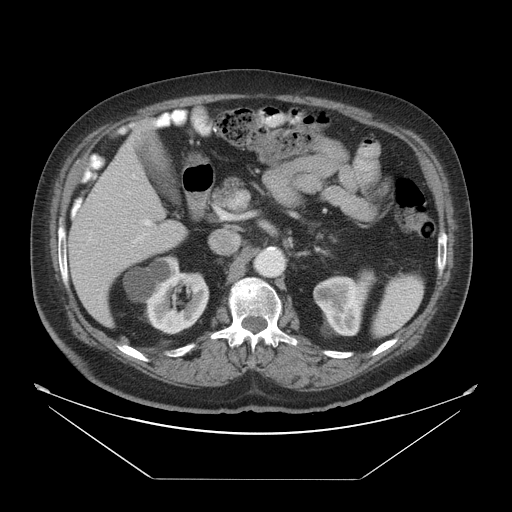
Contrast-enhanced abdominal CT, one axial slice. Position 25 of 45 along the scan axis. 120 kVp. Intravenous contrast given. Soft-tissue window (W 400 / L 40 HU). 5 mm slice thickness. 512 × 512 image matrix. Male patient, age 87 years. Case-level facts recorded for this patient, not image findings: diagnosis: colorectal cancer liver metastases, imaged before liver resection; multiple liver metastases: no; largest metastasis: 4.5 cm.
Structures marked on this image (outlined manually by an expert reader):
- liver: bounding box [x1, y1, x2, y2] px = [68, 138, 187, 327]
- portal vein (with intrahepatic branches): [128, 191, 164, 227]